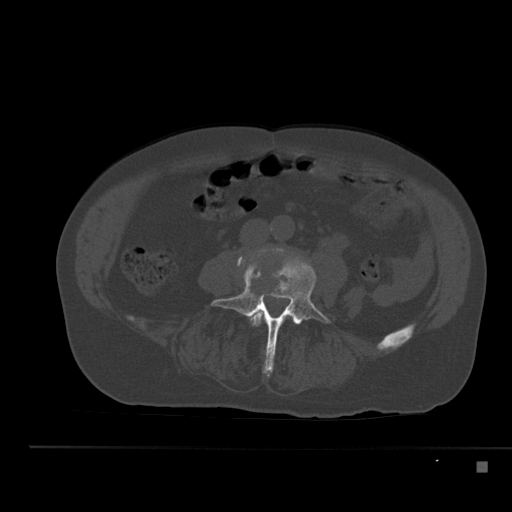
CT including the spine, one axial slice. Reconstruction kernel Br40s. Bone window (W 1800 / L 400 HU). 512 × 512 image matrix. Patient: male, 70 years. Case-level facts recorded for this patient, not image findings: primary cancer: renal; vertebrae with lytic lesions (as recorded): T4, T6, T10, T12, L3, L4, L5.
Outlined on this slice (semi-automatic segmentation, software-assisted and operator-edited):
- L3 vertebra: bounding box <250,310,277,349> (left, top, right, bottom; pixels)
- L4 vertebra: <211,256,331,376>